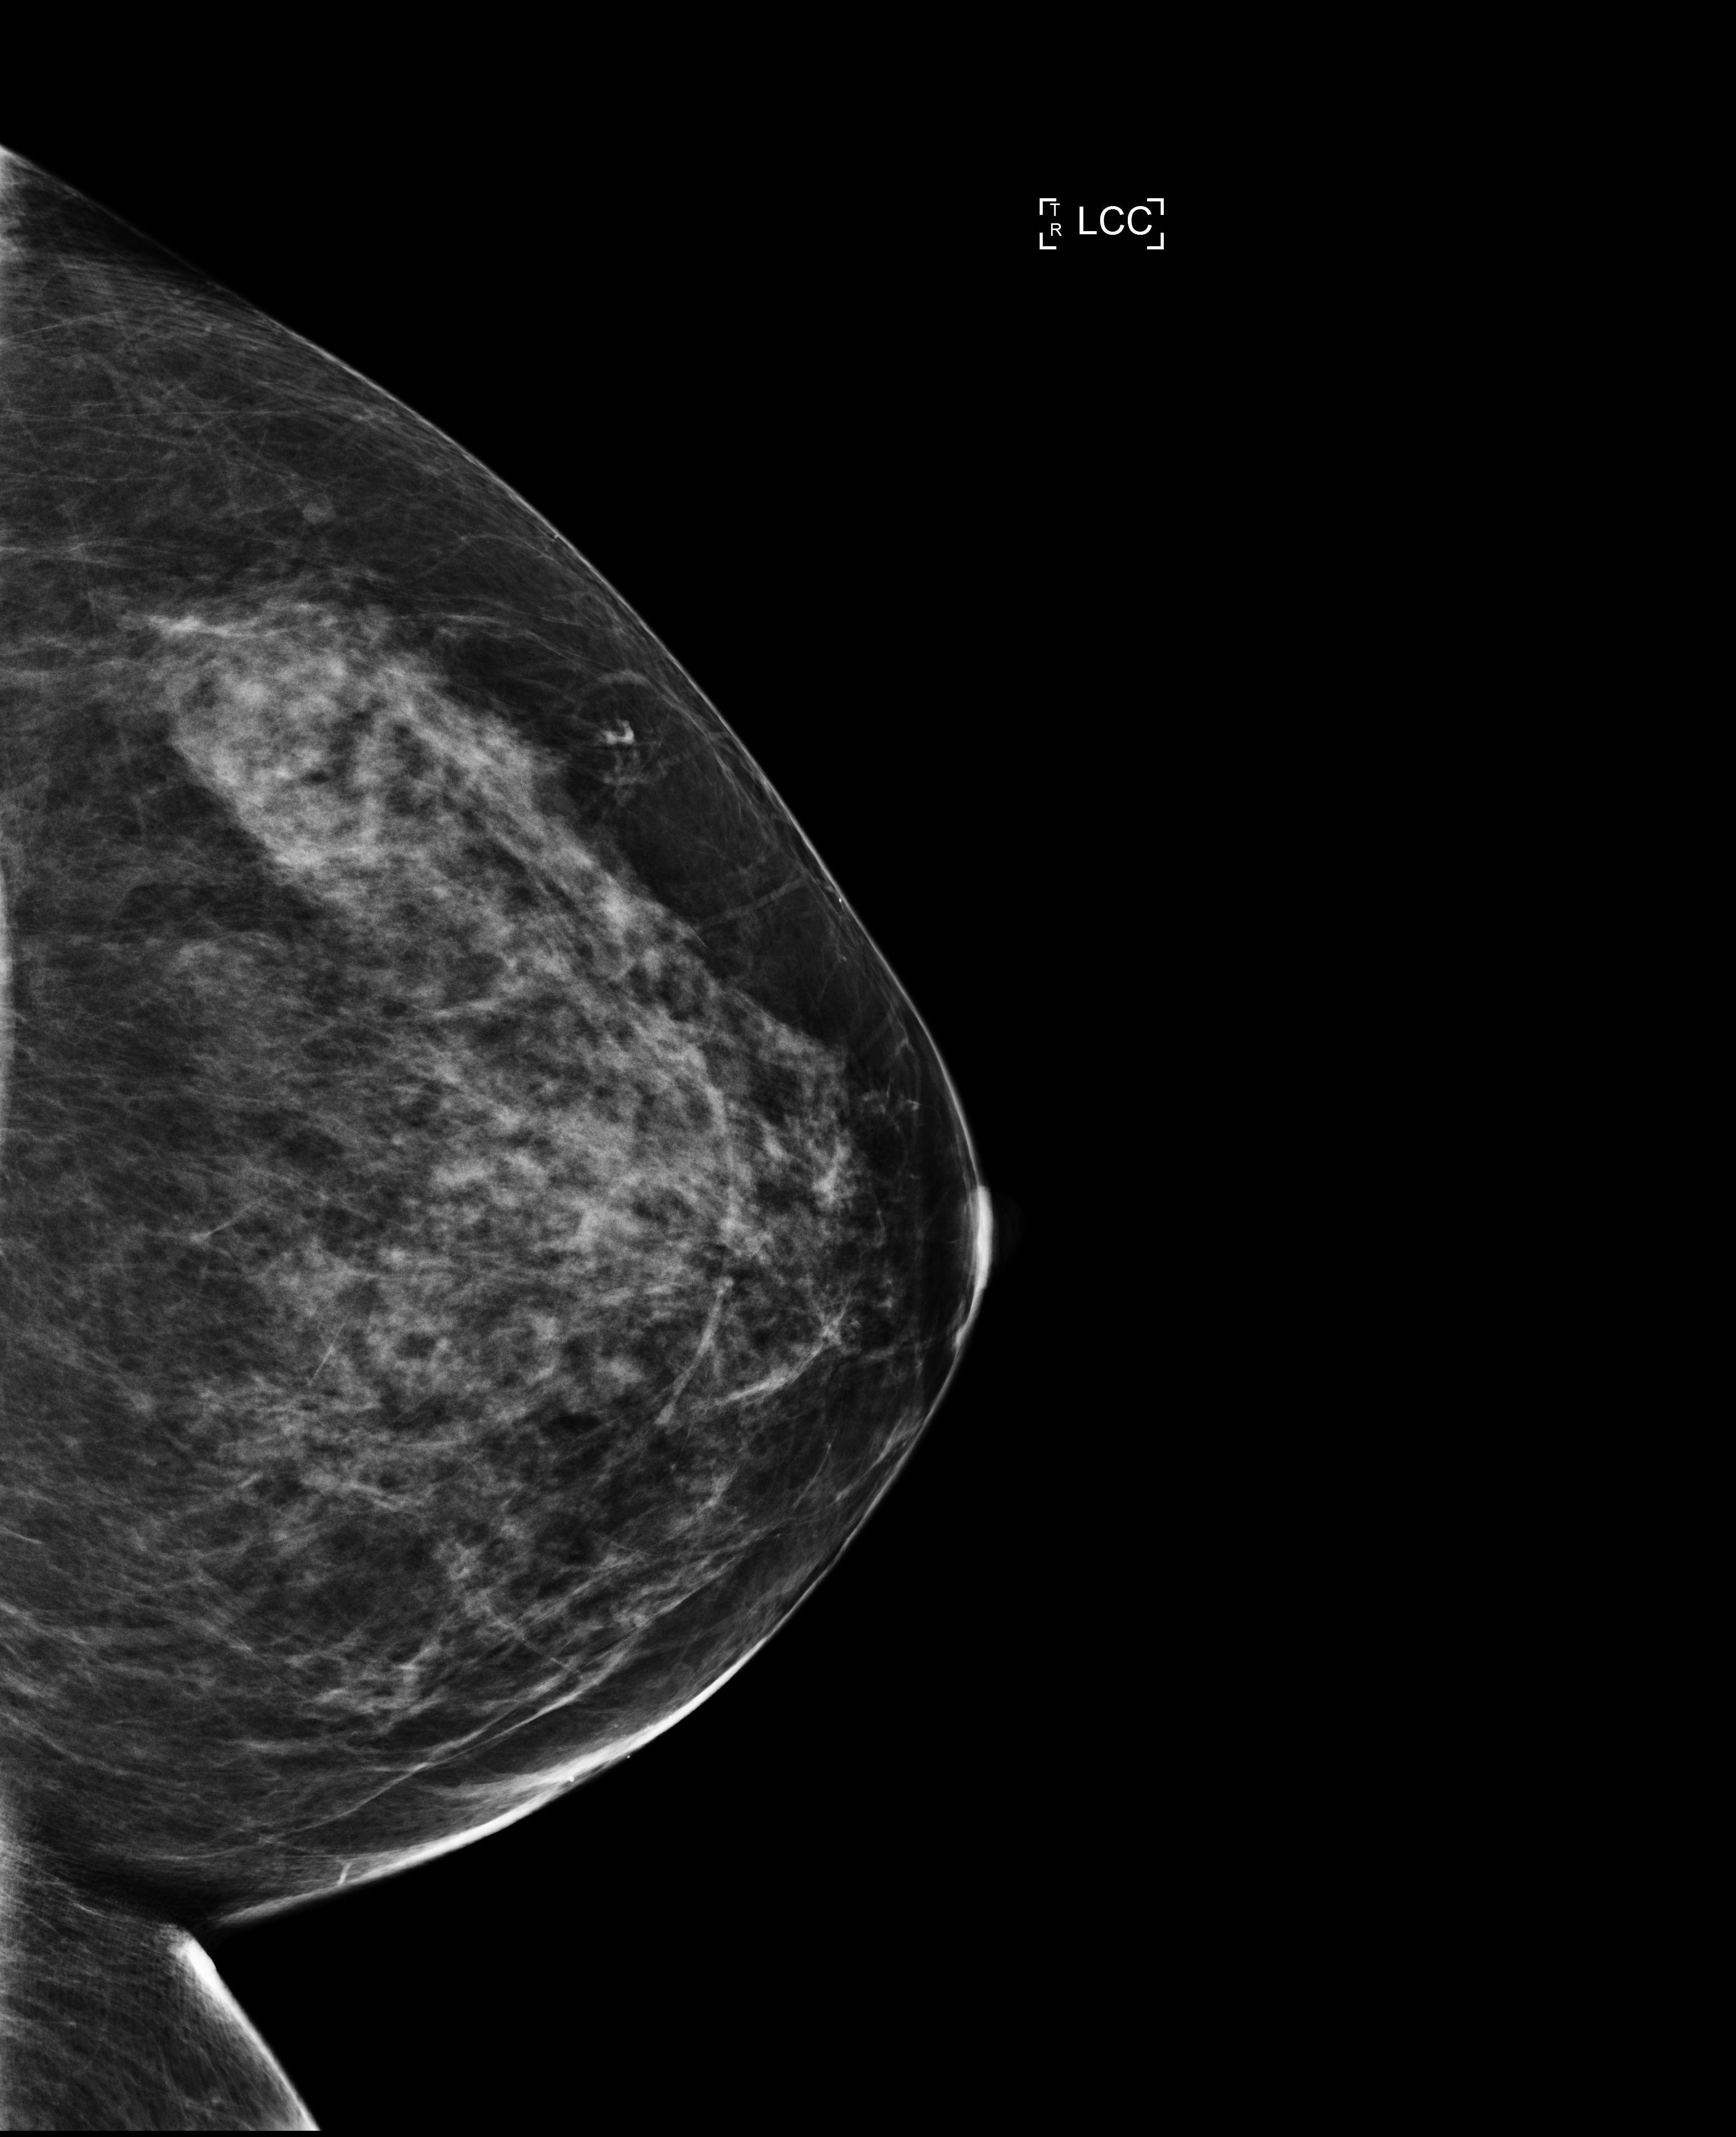
Digital mammogram (FFDM), left breast, cranio-caudal projection, annual screening mammography examination. Female patient, age 46 years.
BI-RADS breast density category at the screening exam (both breasts, scale 1–4): 3. Final BI-RADS assessment for this screening round (tomosynthesis exam, both breasts): category 1. Recall: no recall after this screen.